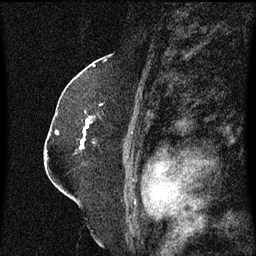
Breast MRI (dynamic contrast-enhanced), one sagittal slice; slice 40 of 60 in the series (ordered by position); dynamic contrast-enhanced series, image 2 of 3 at this slice position (ordered by acquisition); 1.5 T; TE 4.2 ms, TR 8.4 ms; 256 × 256 image matrix, field of view 200 × 200 mm. Patient: female, 52 years. From the clinical record (not read from this slice): setting: breast cancer imaged before/during neoadjuvant chemotherapy; receptor status: HR-positive, HER2-negative.
Structures marked on this image (semi-automatic segmentation, software-assisted and operator-edited):
- analysis volume of interest (the breast-tissue region the enhancement analysis was run in; not a lesion): bounding box <80,104,103,151> (left, top, right, bottom; pixels)
- tumour enhancement mask (voxels above the 70 % enhancement threshold inside the analysis volume of interest): <80,124,89,151>